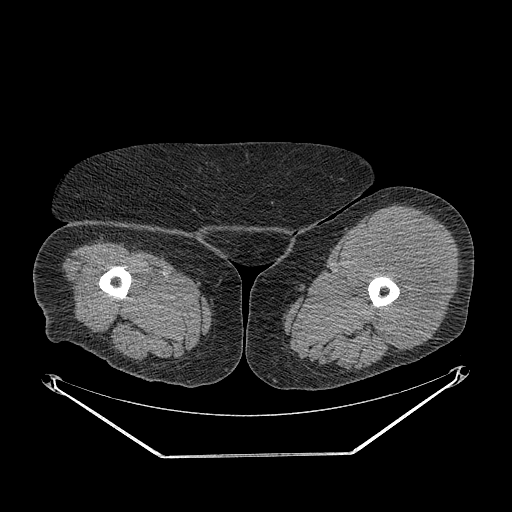
CT of an extremity soft-tissue mass (from a PET/CT study), one axial slice. Reconstruction kernel STANDARD. 140 kVp. Soft-tissue window (W 400 / L 40 HU). 3.75 mm slice thickness. 512 × 512 image matrix, field of view 500 × 500 mm. Female patient. From the clinical record (not read from this slice): histological type: undifferentiated – high grade; grade: high; site of the primary tumour: left thigh.
Structures marked on this image (expert contour drawn on MRI and transferred to this co-registered scan by the dataset authors):
- gross tumour volume including surrounding oedema: bounding box (x1, y1, x2, y2) in pixels: (352, 221, 446, 350)
- gross tumour volume (mass): (352, 221, 446, 350)